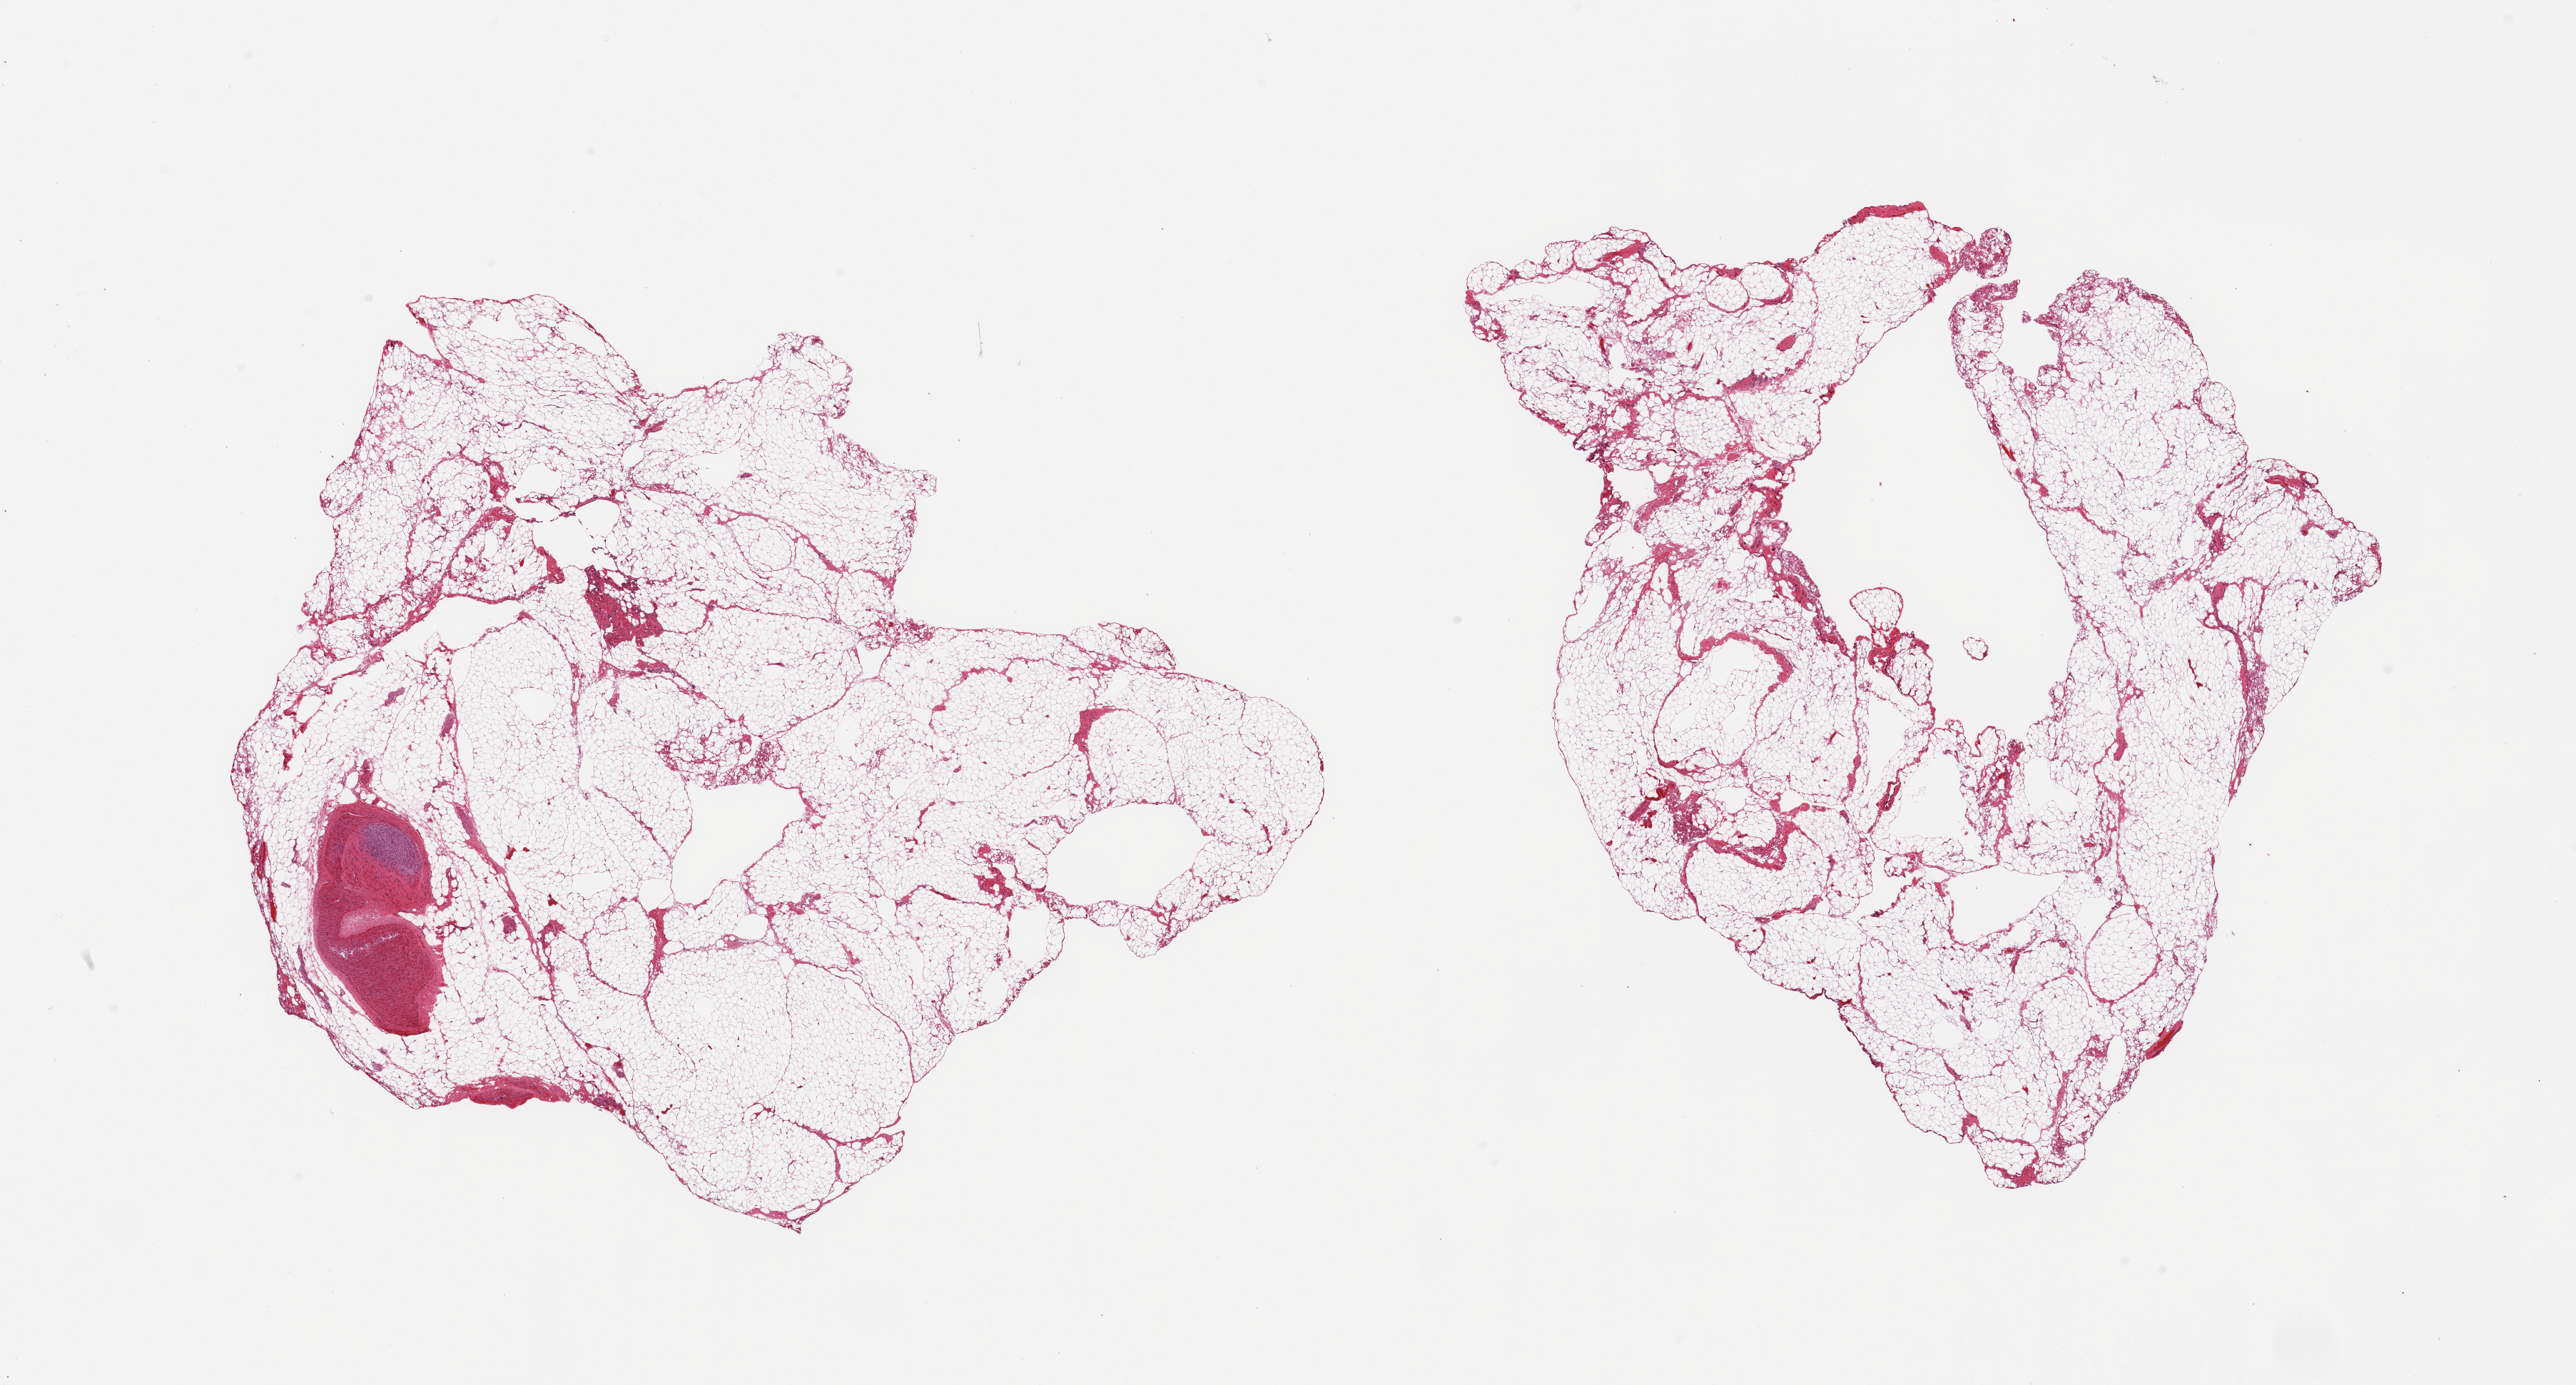
Digitized haematoxylin and eosin-stained section — whole scanned area (about 28.5 x 15.3 mm) shown as a low-resolution overview; PAXgene-fixed paraffin-embedded (PFPE) section; section of omentum (target tissue); donor tissue sample. Donor sex: male.
- reviewer comment on this tissue sample: 2 pieces; lobulated mature adipose tissue with prominent congested fibrovascular component and larger vessel wall